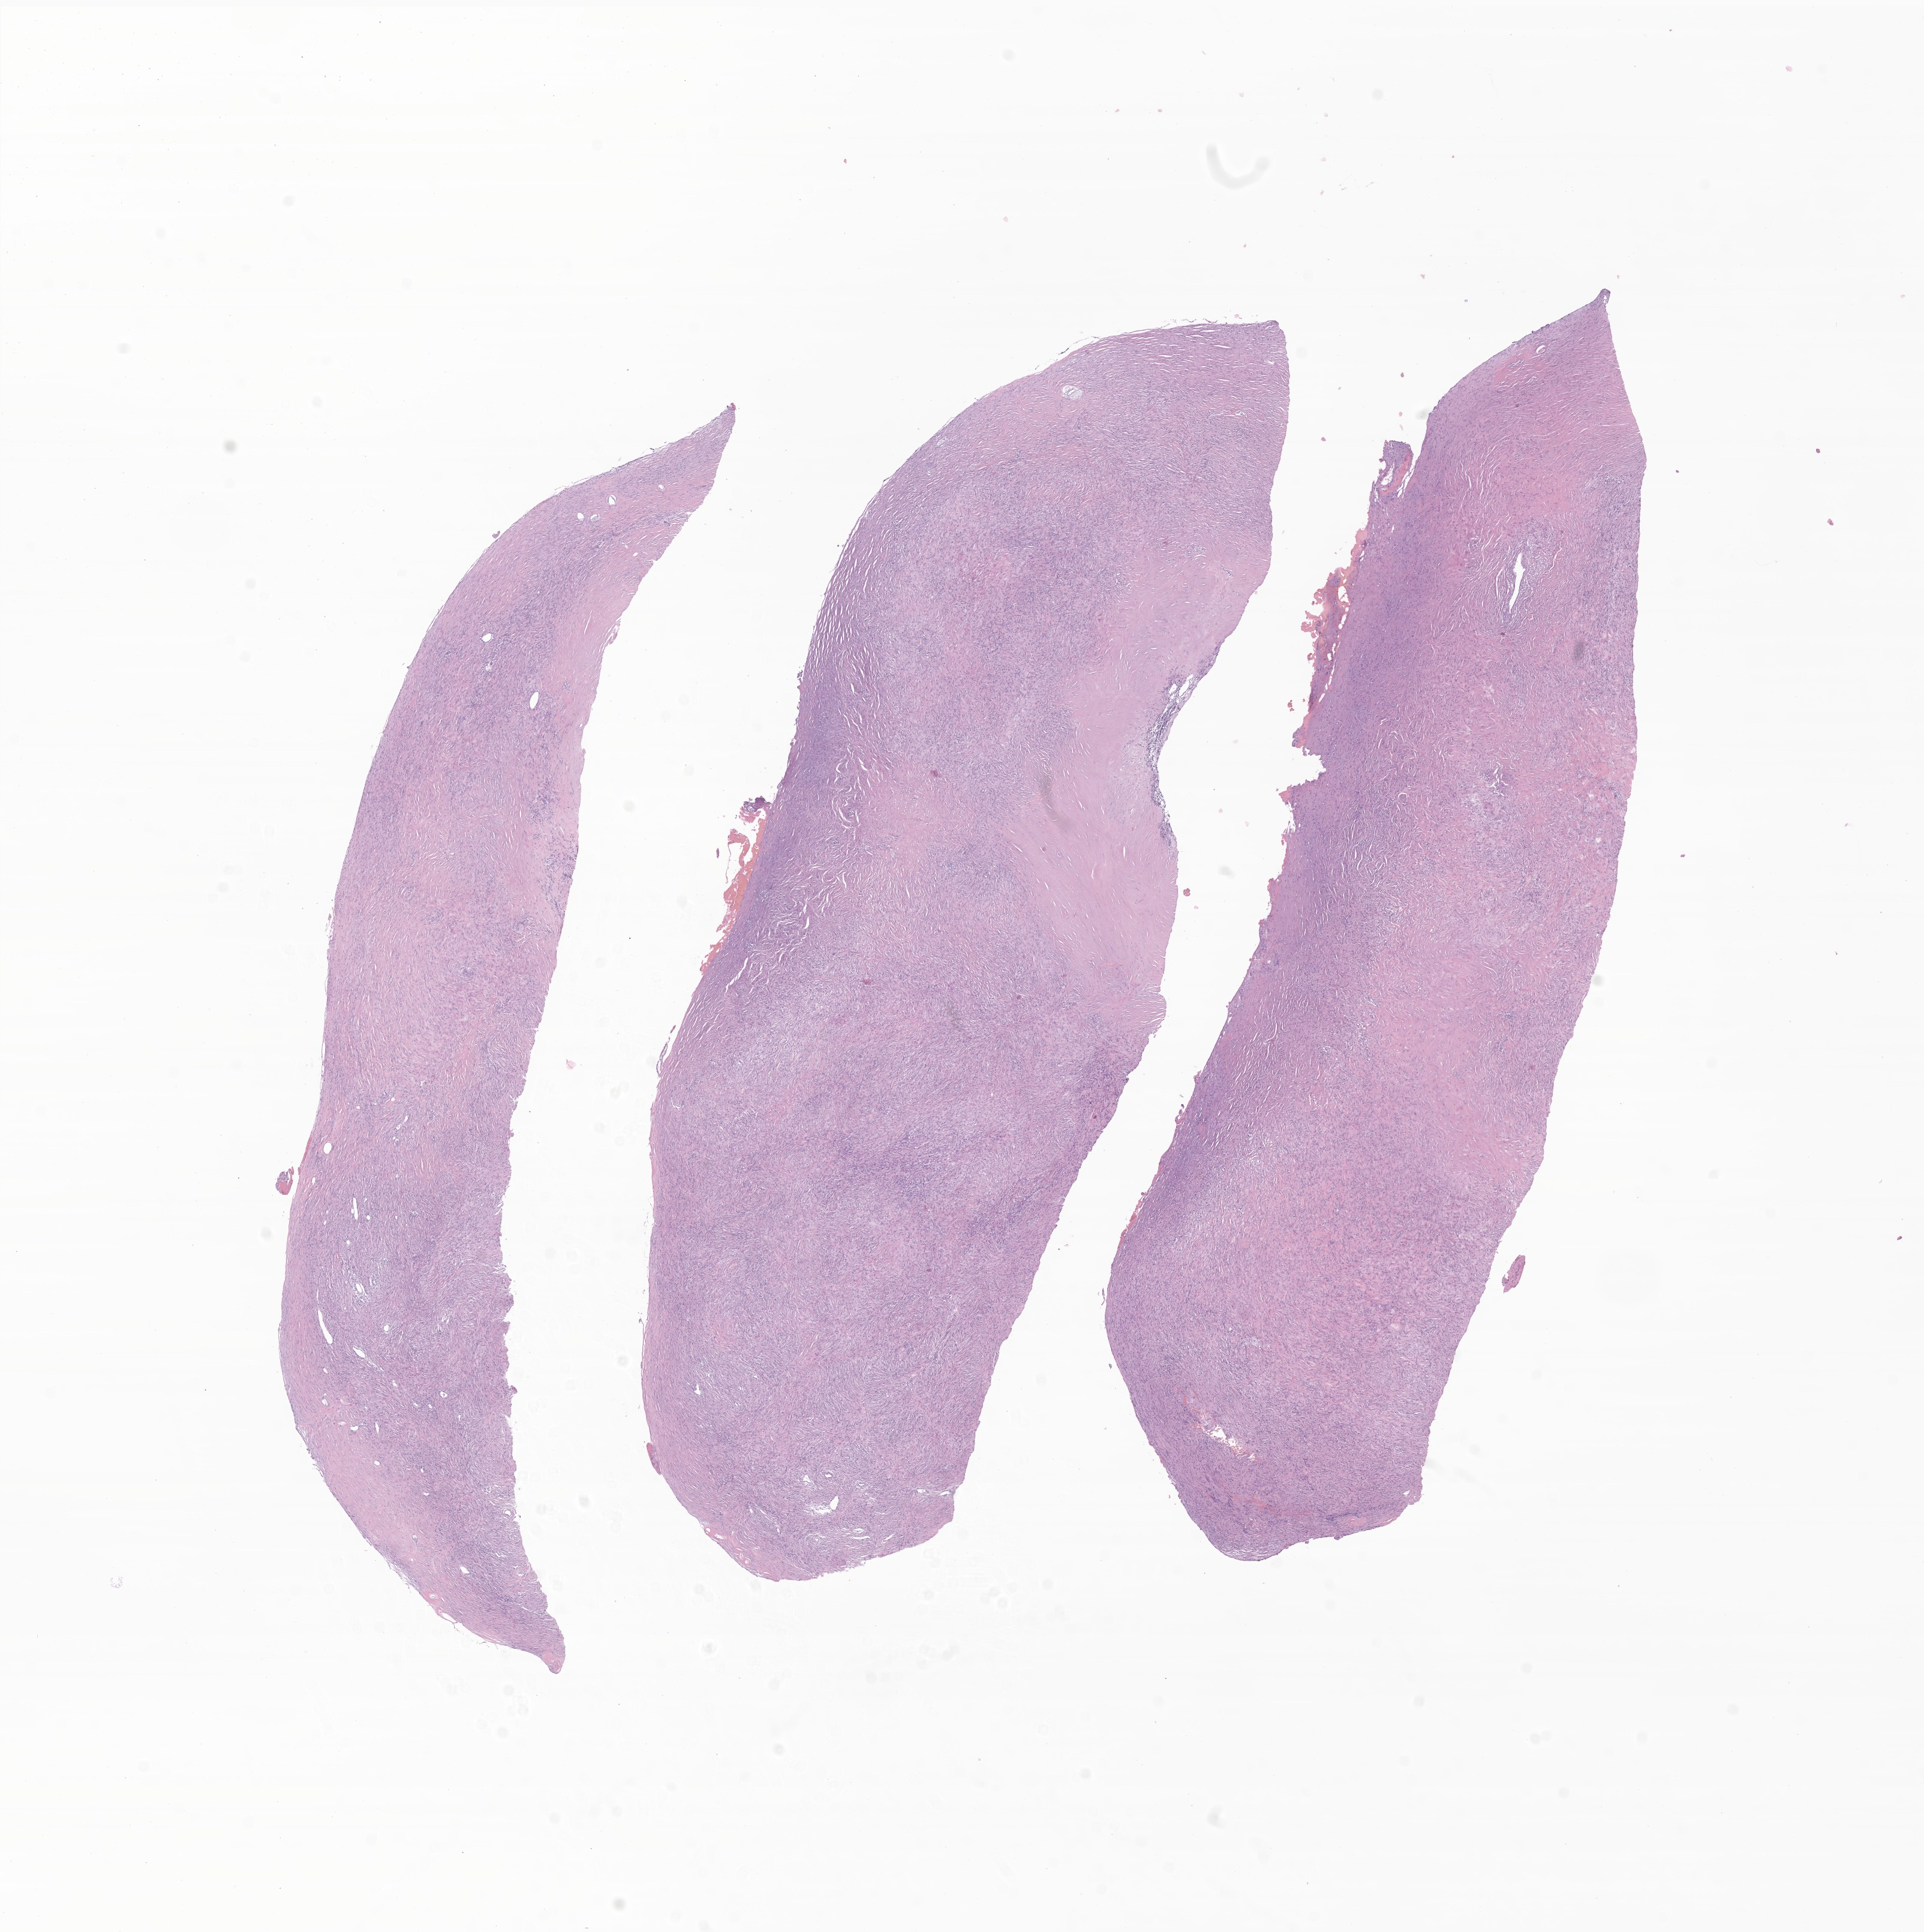
Digitized hematoxylin and eosin (H&E)-stained section of tumor tissue from the brain, a low-resolution overview of the entire scanned area, about 13.5 x 13.6 mm, formalin-fixed, paraffin-embedded (FFPE) tissue. Female patient, age 142 months (11 years 10 months).
* diagnosis: Meningioma, NOS